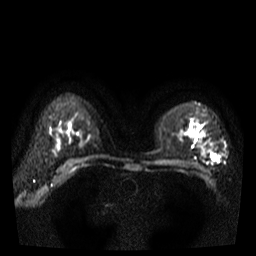
Breast MRI, one axial slice. Slice 27 of 38 in the series (ordered by position). Diffusion-weighted series; image 2 of 4 stored at this slice position (different b-values; order by instance number). 3 T. 5 mm slice thickness. 256 × 256 image matrix. Female patient.
Outlined on this slice (manually delineated by an expert):
- tumour on diffusion-weighted imaging: bounding box [x1, y1, x2, y2] px = [211, 154, 217, 161]